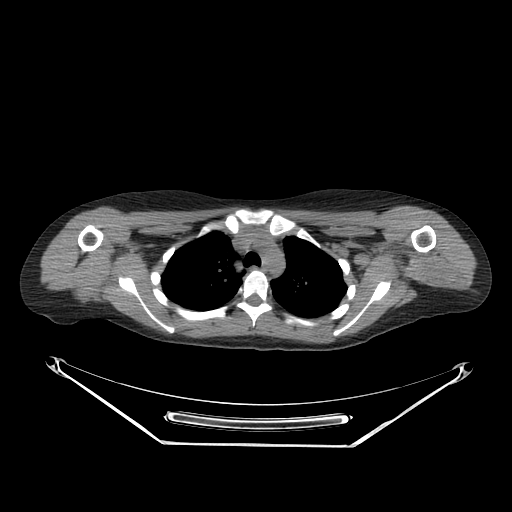
CT of an extremity soft-tissue mass (from a PET/CT study), one axial slice. Position 206 of 267 along the scan axis. Reconstruction kernel SOFT. Soft-tissue window (W 400 / L 40 HU). 512 × 512 image matrix, field of view 500 × 500 mm. Female patient. From the clinical record (not read from this slice): histological type: malignant fibrous histiocytoma; grade: low; site of the primary tumour: left arm.
Annotated regions visible in this slice (expert contour drawn on MRI and transferred to this co-registered scan by the dataset authors):
- gross tumour volume (mass): bounding box [x1, y1, x2, y2] px = [420, 249, 458, 284]